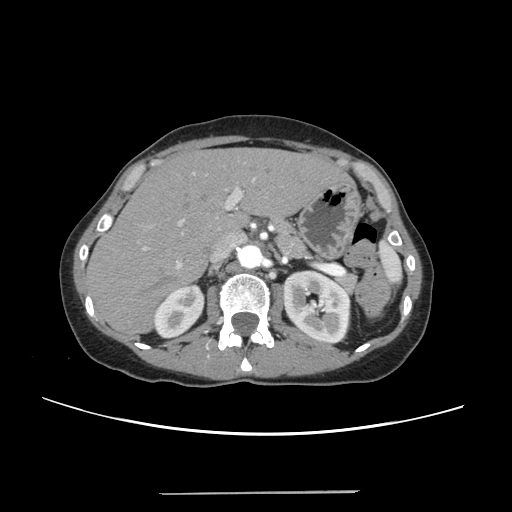
Contrast-enhanced abdominal CT, one axial slice; position 156 of 240 along the scan axis; 120 kVp; intravenous contrast given; soft-tissue window (W 400 / L 40 HU); 512 × 512 image matrix, field of view 371 × 371 mm. Female patient, age 60 years. Case-level facts recorded for this patient, not image findings: diagnosis: colorectal cancer liver metastases, imaged before liver resection; multiple liver metastases: no; largest metastasis: 1.5 cm.
Annotated regions visible in this slice (expert manual segmentation):
- liver: bounding box [x1, y1, x2, y2] px = [89, 149, 347, 333]
- planned liver remnant (the part of the liver to remain after resection): [89, 149, 345, 332]
- portal vein (with intrahepatic branches): [144, 171, 257, 268]